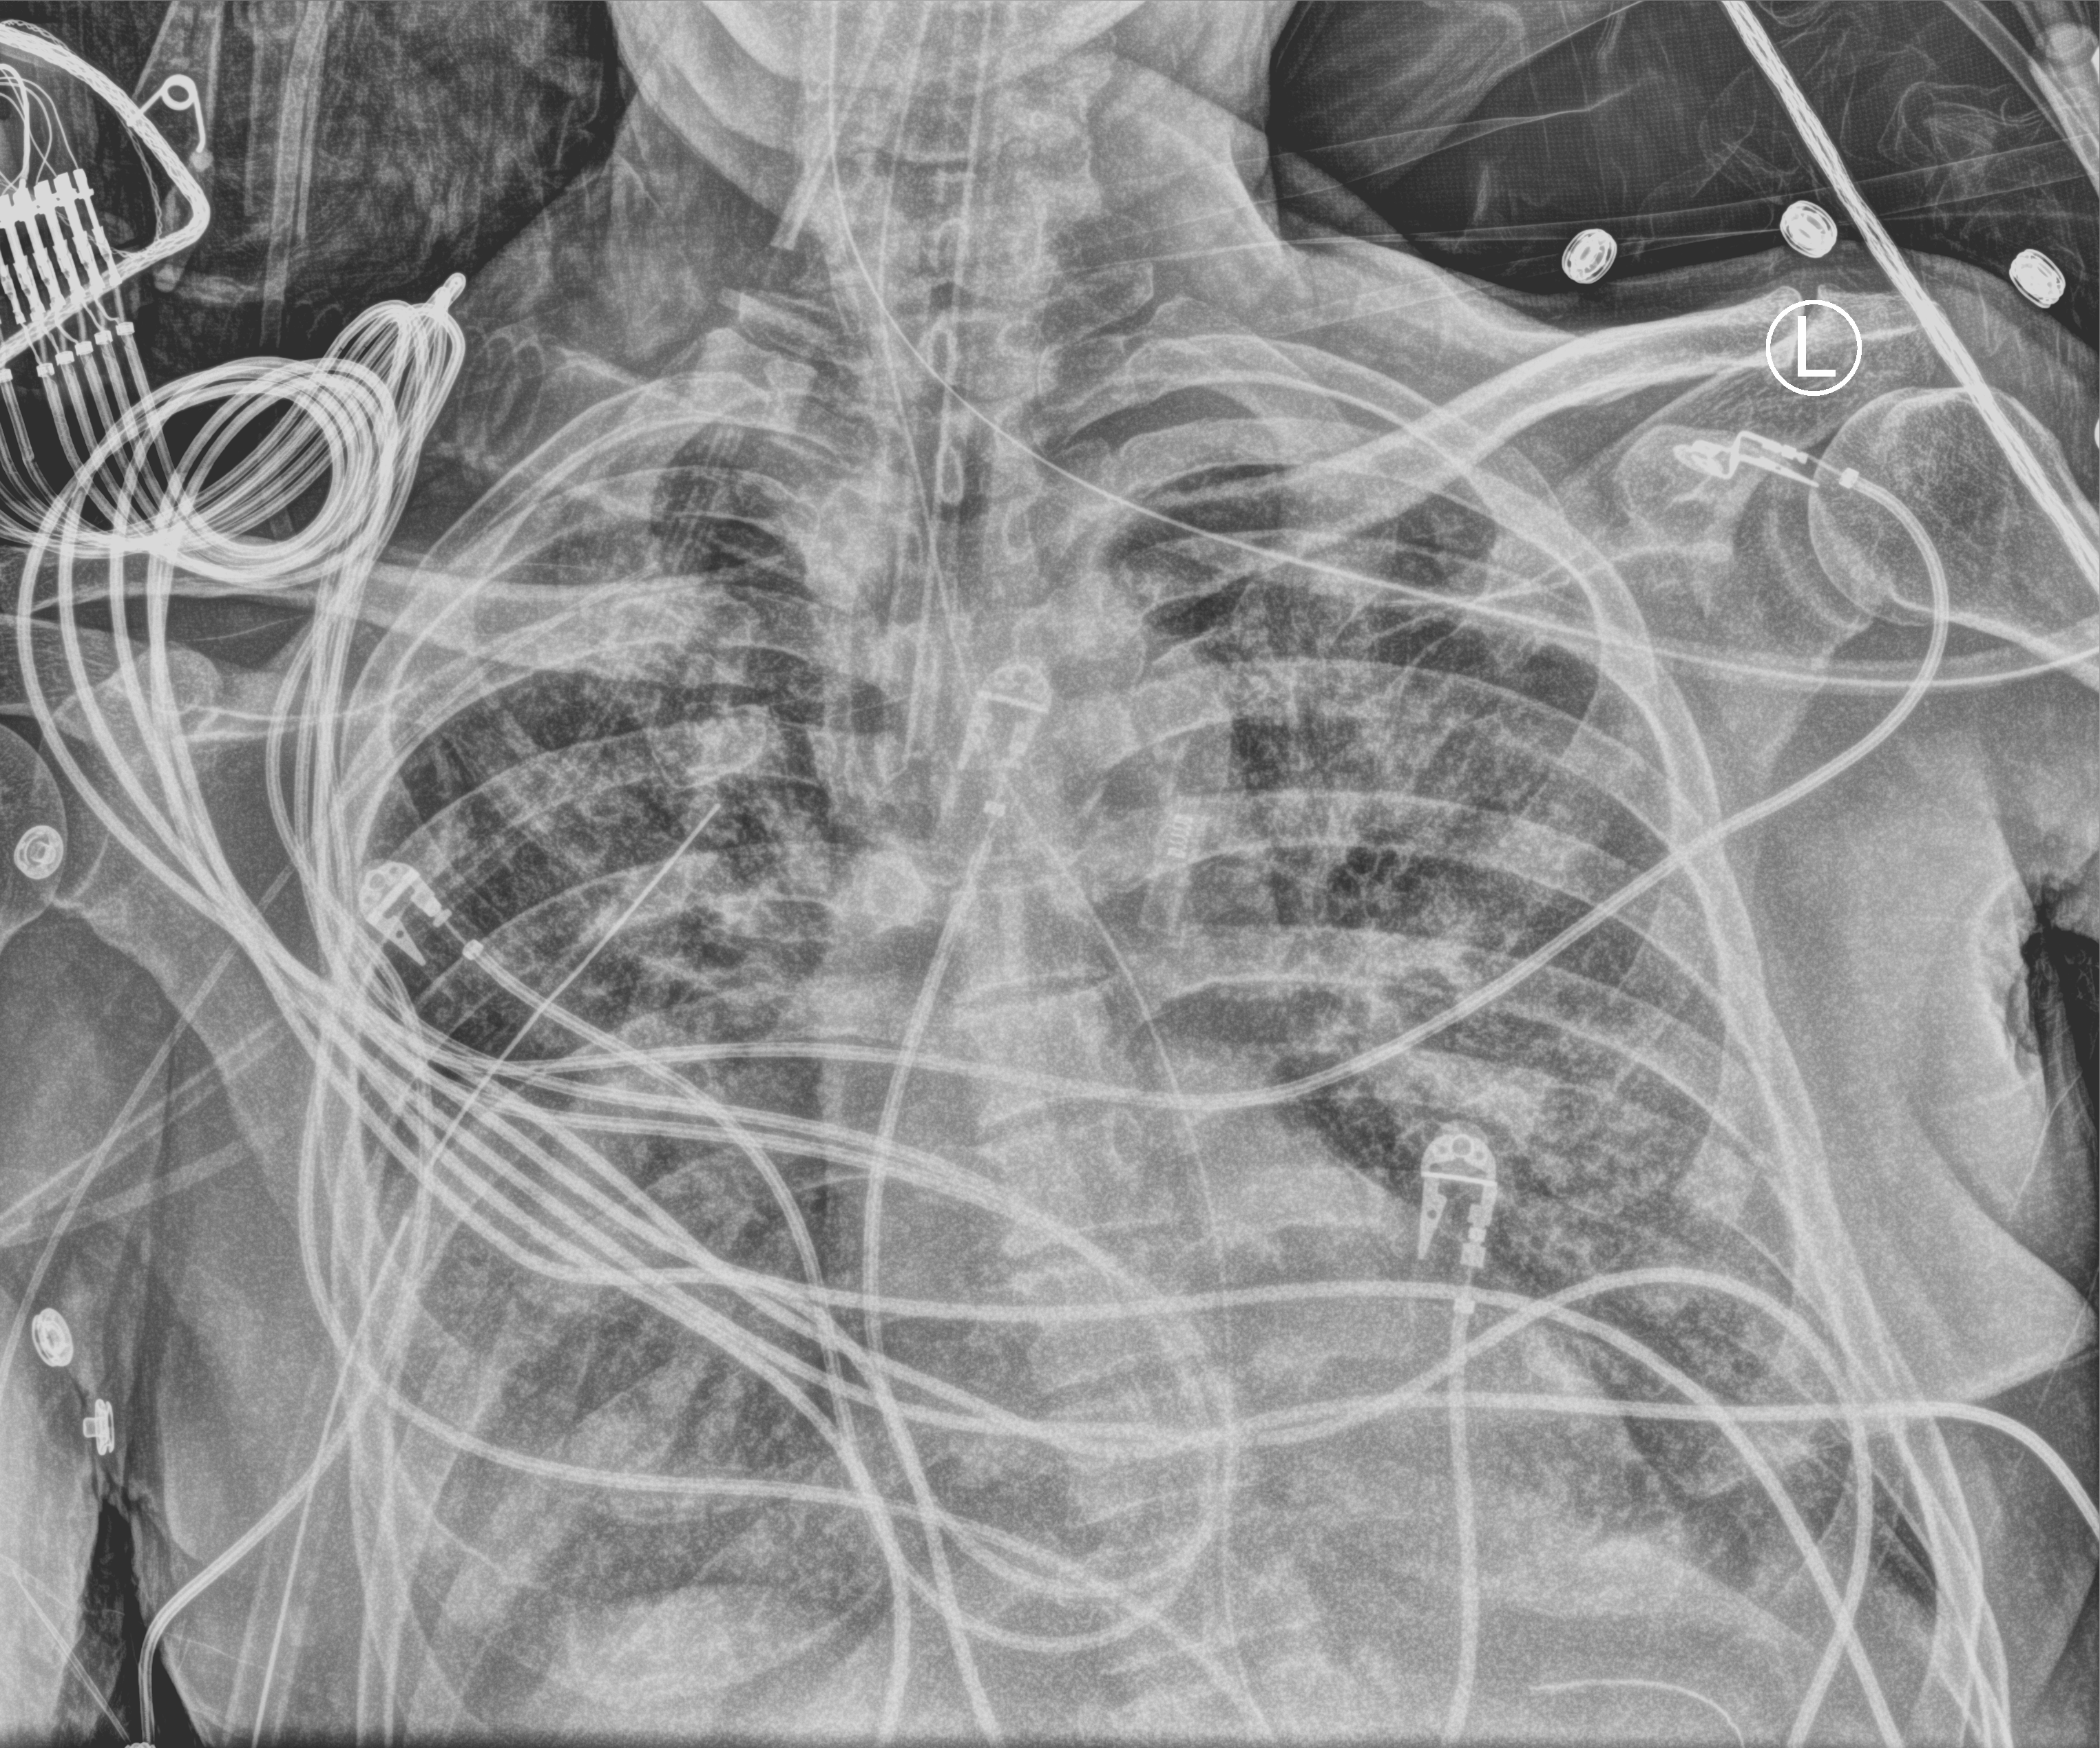
Portable chest radiograph, anteroposterior (AP) projection. Male patient hospitalised with COVID-19, age 60–74 years.
From the hospital-stay record, not from the radiograph (when in the stay this image was taken is not recorded):
- smoking status (admission record): former
- mechanically ventilated during this hospital stay: yes
- hypertension (admission record): no